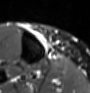
MRI of an extremity soft-tissue mass, one axial slice. Slice 16 of 60 in the series (ordered by position). STIR. MR volume resampled by the dataset authors to the PET/CT grid (not the native acquisition matrix). 90 × 93 image matrix. Female patient. From the clinical record (not read from this slice): histological type: undifferentiated – high grade; grade: high; site of the primary tumour: right thigh.
Outlined on this slice (expert contour drawn on MRI and transferred to this co-registered scan by the dataset authors):
- gross tumour volume (mass): bounding box [x1, y1, x2, y2] px = [37, 31, 54, 52]